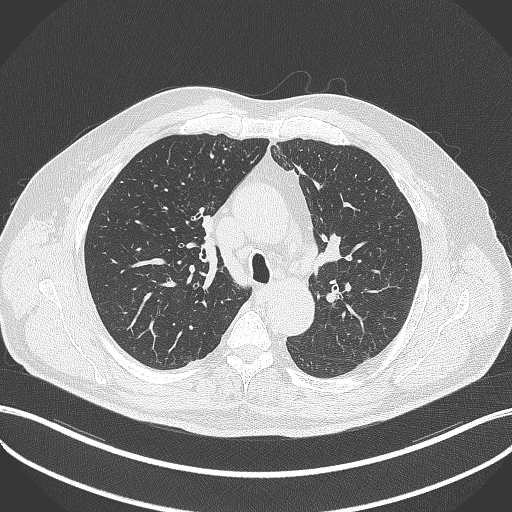
Chest CT, one axial slice; position 259 of 411 along the scan axis; 120 kVp; lung window (W 1500 / L -600 HU); 1 mm slice thickness; 512 × 512 image matrix, field of view 400 × 400 mm. Patient: male, 60 years. From the clinical record (not read from this slice): clinical TNM (as recorded): T1b N1 M0.
Outlined on this slice (rectangle marked by the reading radiologist):
- lung tumour (recorded histology: squamous cell carcinoma): bounding box (x1, y1, x2, y2) in pixels: (201, 214, 213, 238)